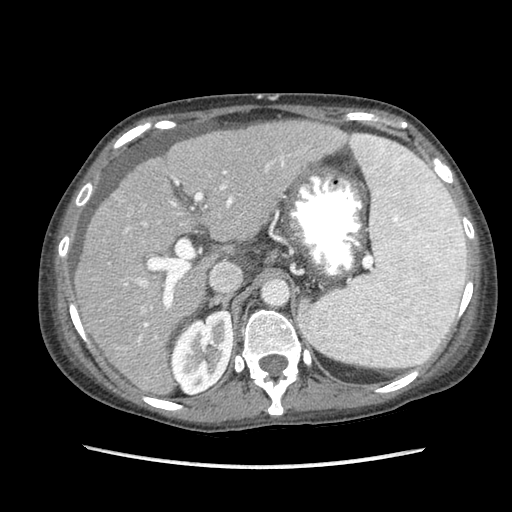
Contrast-enhanced abdominal CT (liver protocol), one axial slice; position 56 of 87 along the scan axis; 120 kVp; soft-tissue window (W 400 / L 40 HU); 2.5 mm slice thickness; 512 × 512 image matrix, field of view 340 × 340 mm. From the clinical record (not read from this slice): diagnosis: hepatocellular carcinoma (patient treated with transarterial chemoembolisation; whether this scan precedes or follows treatment is not stated here); TNM stage (as recorded): Stage-IIIB; Child-Pugh class: A; tumour differentiation: no biopsy; tumour nodularity: uninodular.
Structures marked on this image (semi-automatically segmented with operator editing):
- liver parenchyma outside the tumour (the mass and vessels are separate outlines, so this box may not span the whole liver): bounding box <74,120,381,394> (left, top, right, bottom; pixels)
- mass: <105,196,134,224>
- liver vessels: <125,135,381,341>